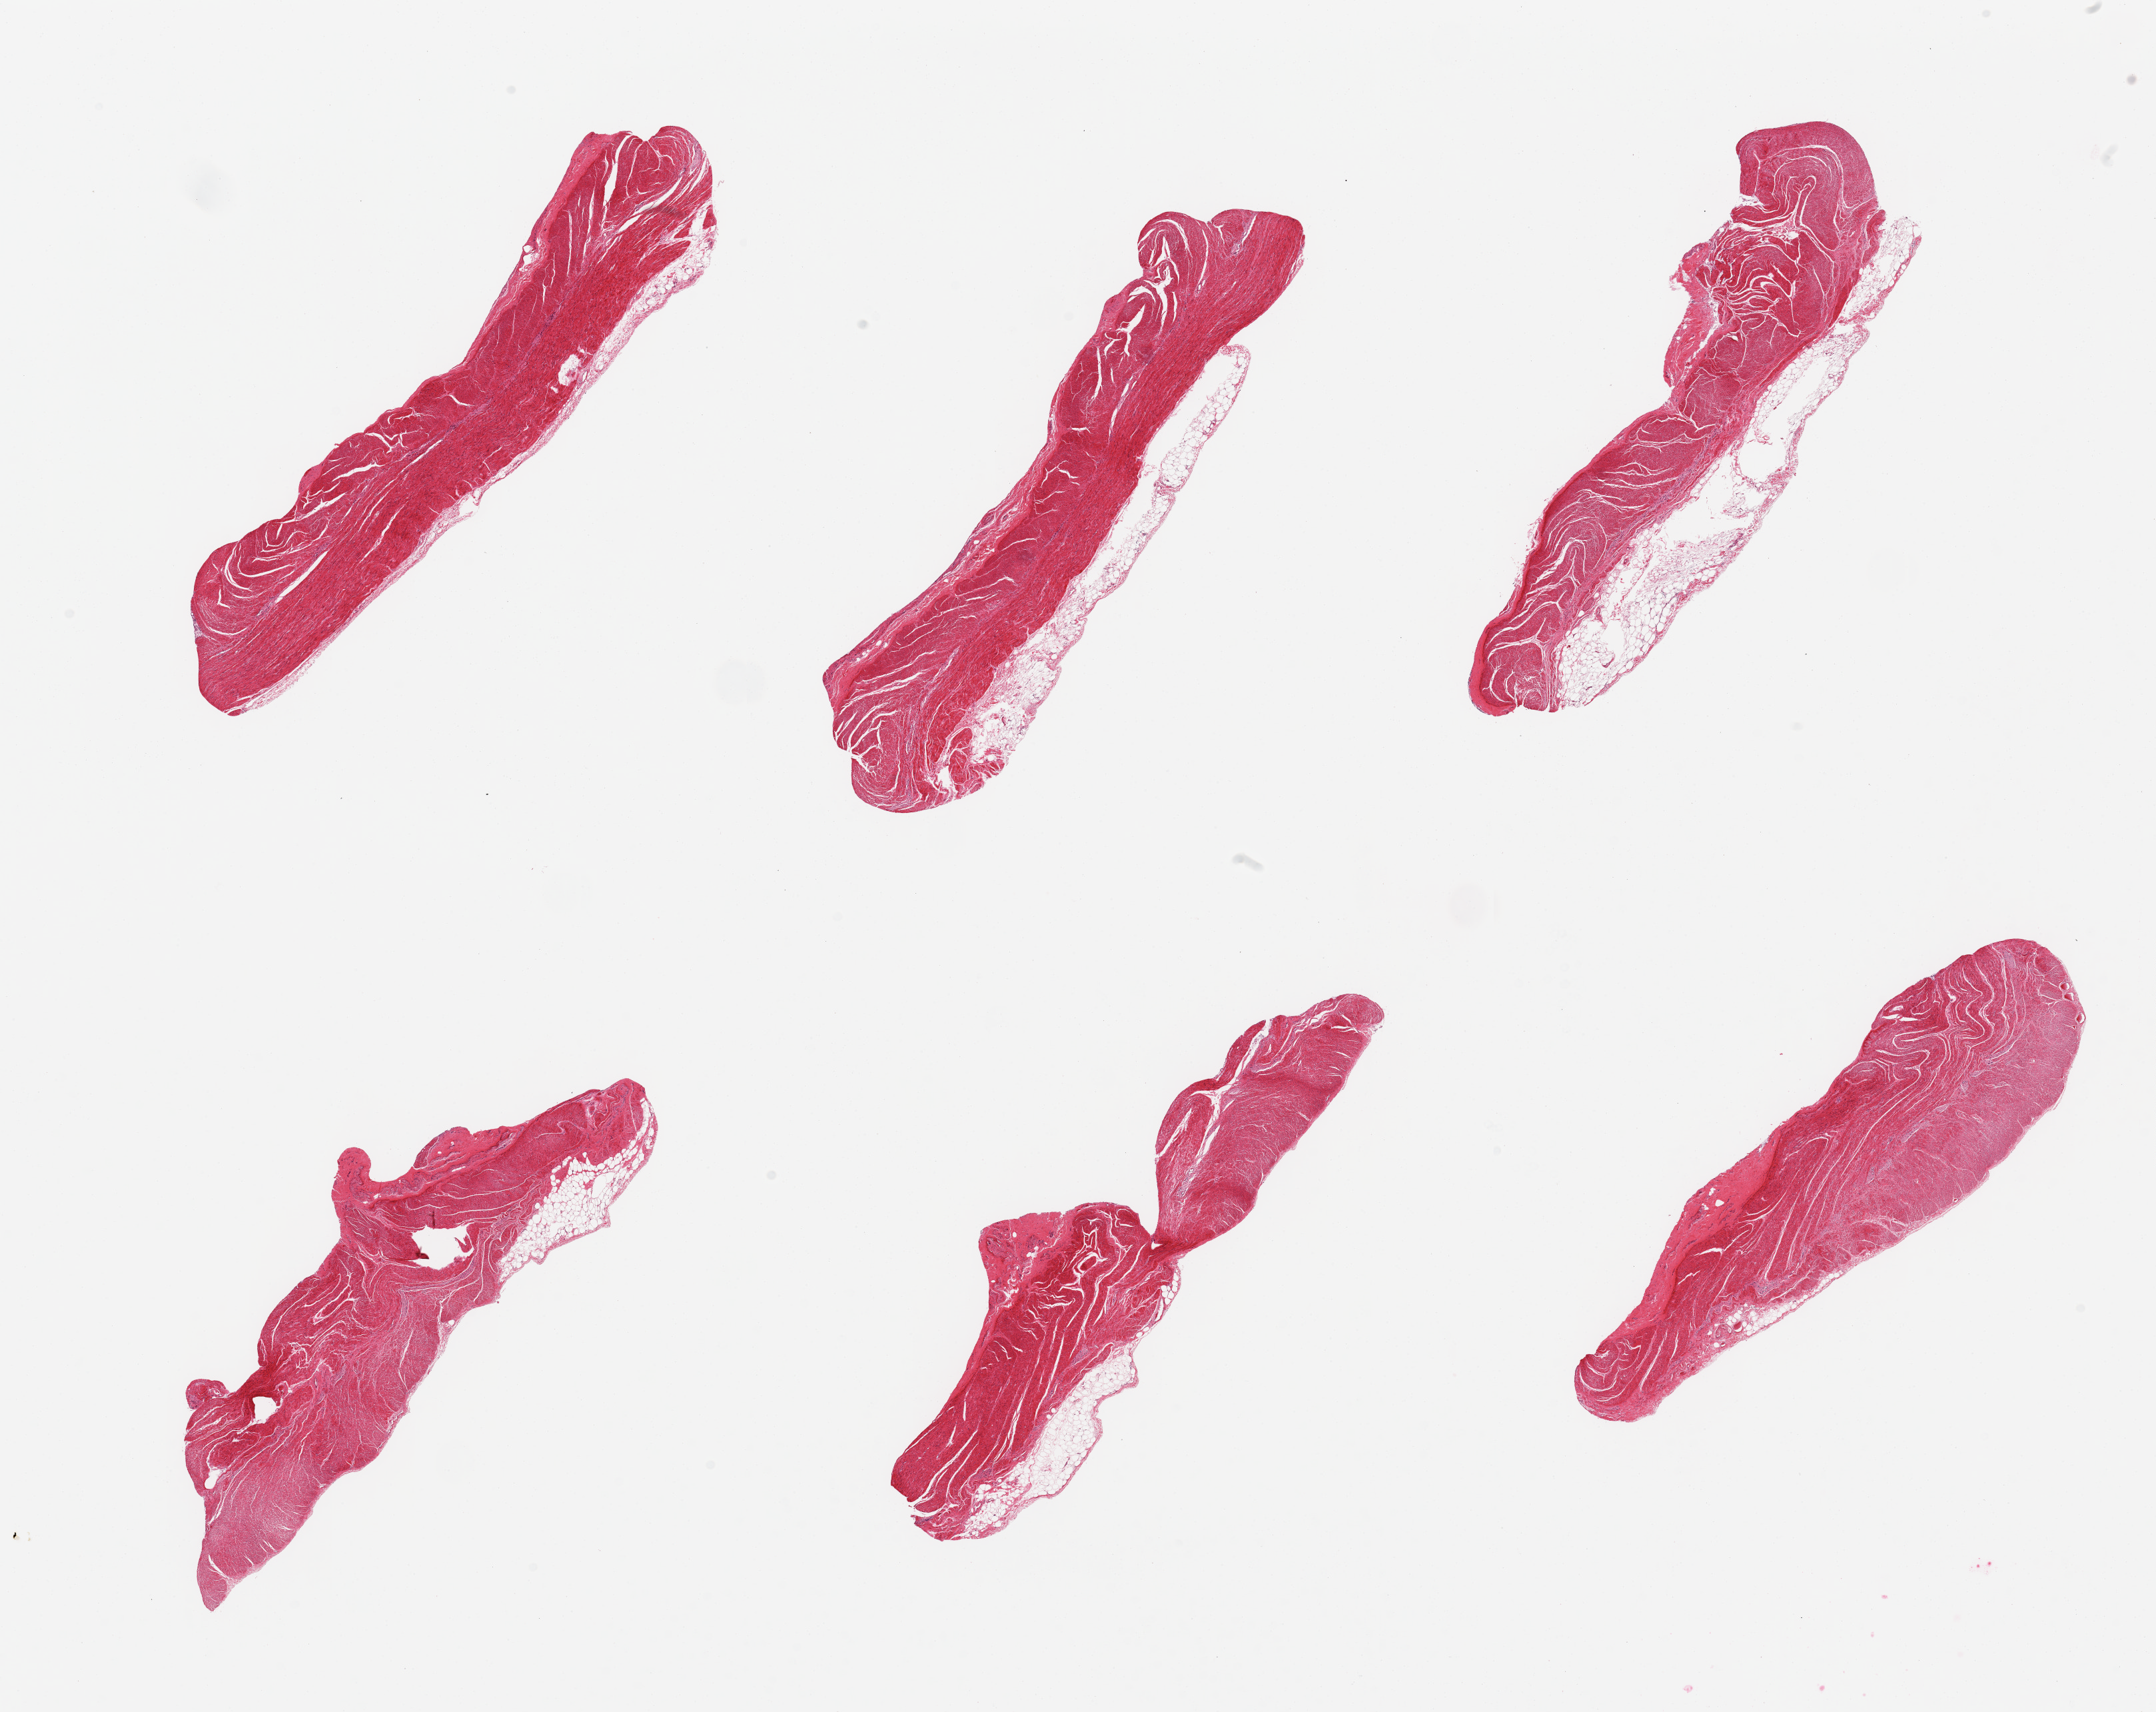
Whole-slide image, H&E stain, brightfield, a low-resolution overview of the entire scanned area, about 25.6 x 20.3 mm. PAXgene-fixed, paraffin-embedded tissue. Section of sigmoid colon (target tissue). Donor tissue sample.
• review note (as recorded): 6 pieces, all muscularis, adherent fat up to ~1mm on some sections